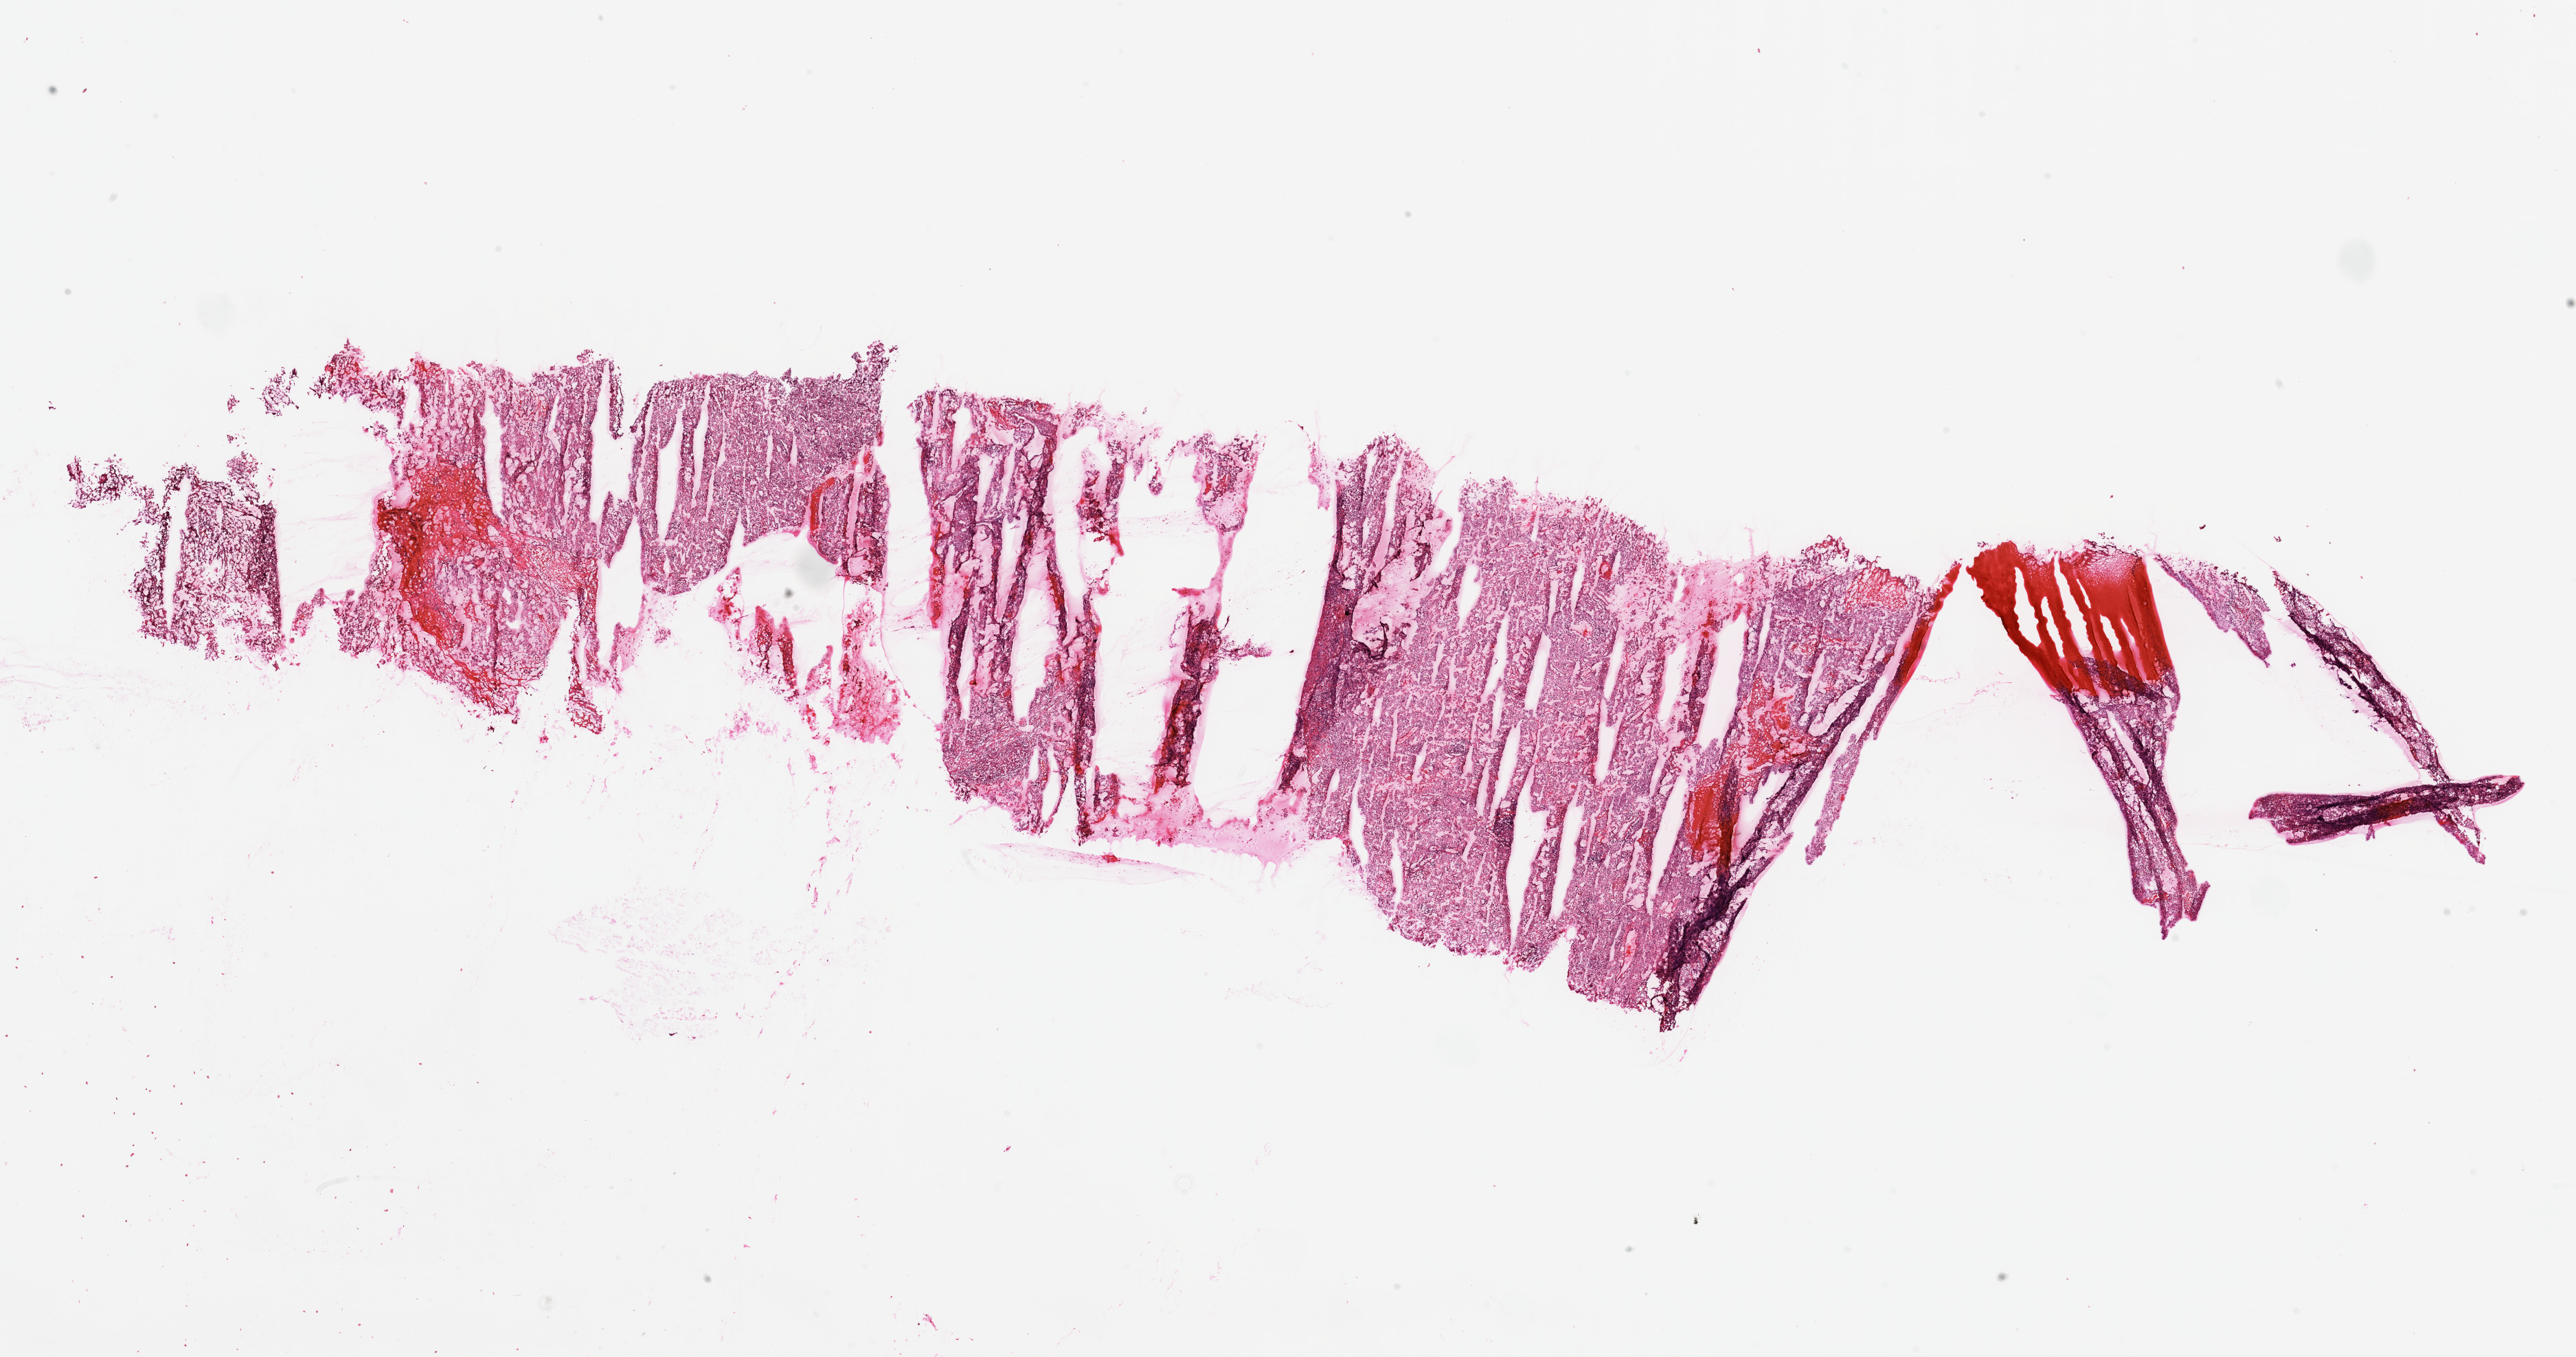
Digitized H&E-stained tissue section (whole slide), shown as a low-resolution overview of the whole scanned area (about 30.1 x 15.8 mm, slide scanned at 20x); frozen section; primary tumour sample from the kidney. Male patient; age at initial diagnosis 47 years. Histologic grade: G3 (poorly differentiated). Pathologist review of this section (percent, as recorded): tumour cells 95%, tumour nuclei 85%, normal cells 0%, stromal cells 5%, necrosis 0%.
AJCC pathologic stage: III. Diagnosis: Clear cell adenocarcinoma, NOS.